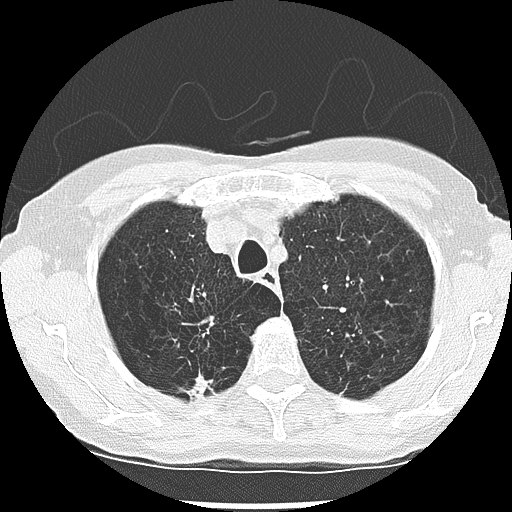
Low-dose screening chest CT, one axial slice; slice 221 of 265 in the series (ordered by position); 120 kVp; lung window (W 1500 / L -600 HU); 2.5 mm slice thickness; 512 × 512 image matrix, field of view 300 × 300 mm.
Structures marked on this image (manually delineated by an expert):
- lesion 1 (nodule, upper lobe of right lung): box from (x=187, y=375) to (x=211, y=399) px